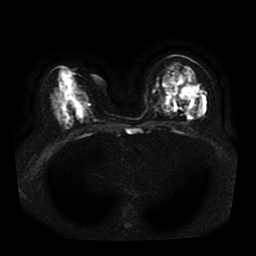
Breast MRI, one axial slice; position 18 of 41 along the scan axis; diffusion-weighted series; image 2 of 4 stored at this slice position (different b-values; order by instance number); 1.5 T; 5 mm slice thickness; 256 × 256 image matrix, field of view 330 × 330 mm. Female patient.
Annotated regions visible in this slice (manually delineated by an expert):
- tumour on diffusion-weighted imaging: box from (x=180, y=85) to (x=203, y=114) px